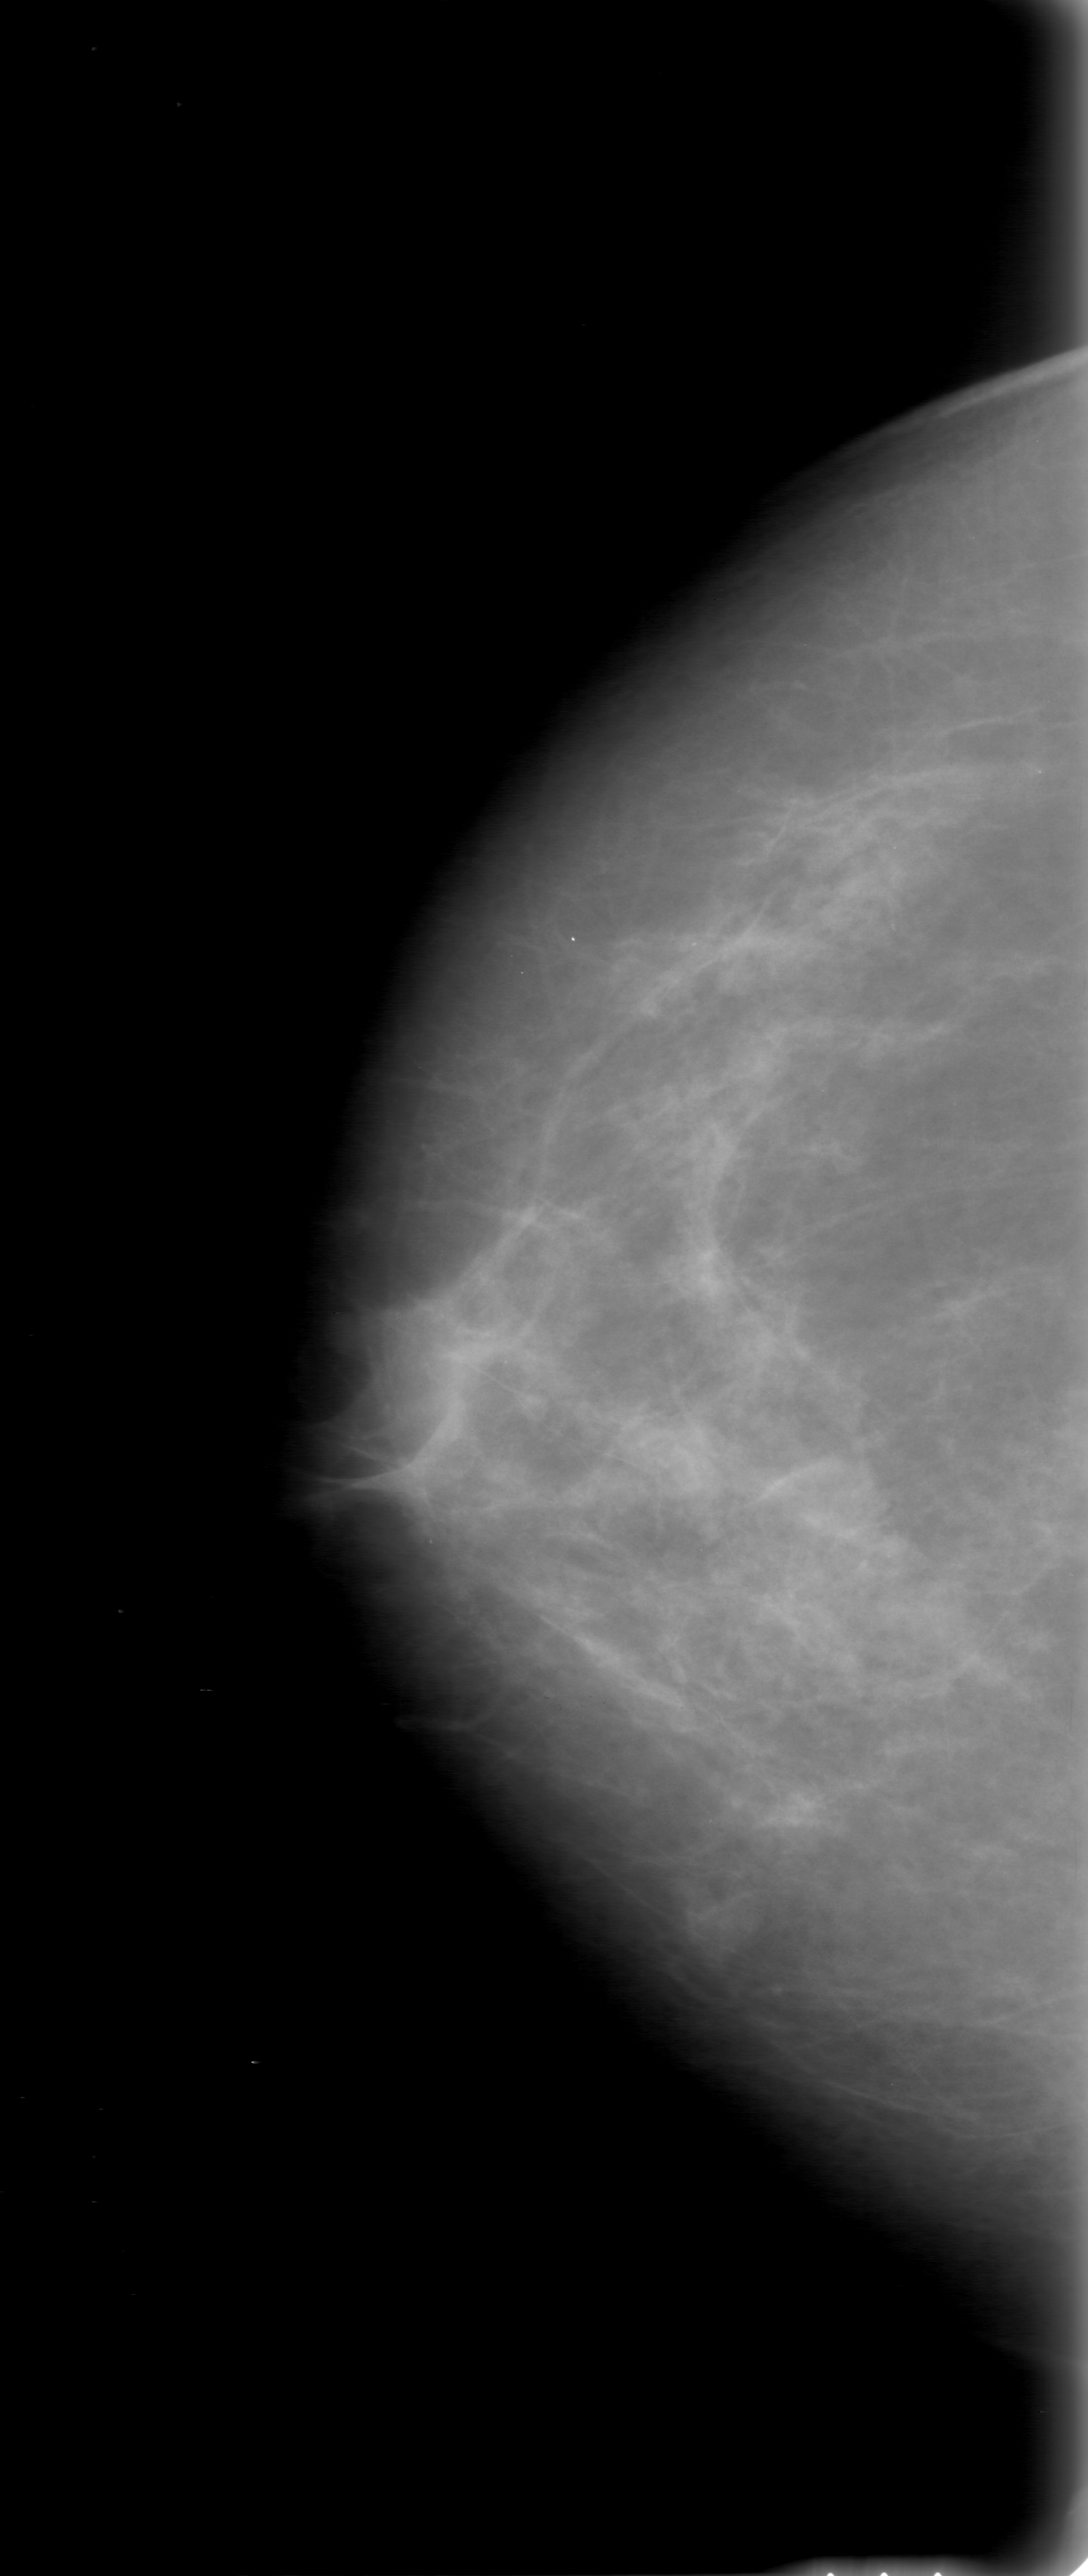
Digitized screen-film mammogram; right breast; CC view; BI-RADS breast density category 2 (scale 1–4).
Abnormality record for this image: mass, shape oval, margins obscured; BI-RADS assessment category 0; pathology result (as recorded, not read from the image): benign.